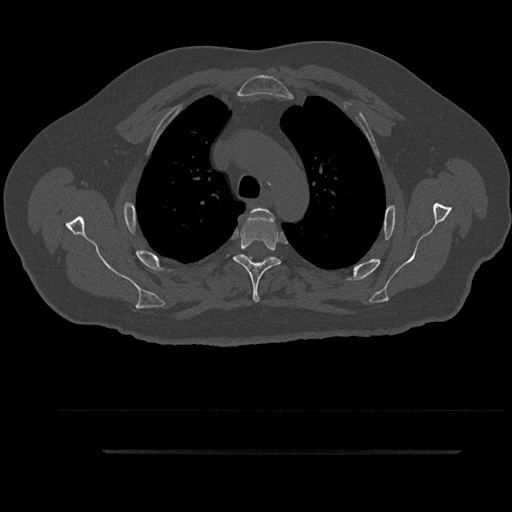
CT including the spine, one axial slice; position 672 of 797 along the scan axis; reconstruction kernel Br40s/3; bone window (W 1800 / L 400 HU); 0.5 mm slice thickness; 512 × 512 image matrix, field of view 432 × 432 mm. Male patient, age 63 years. Case-level facts recorded for this patient, not image findings: primary cancer: renal; vertebrae with lytic lesions (as recorded): T8.
Outlined on this slice (semi-automatic segmentation, software-assisted and operator-edited):
- T3 vertebra: bounding box (x1, y1, x2, y2) in pixels: (247, 208, 273, 264)
- T4 vertebra: (234, 211, 281, 302)